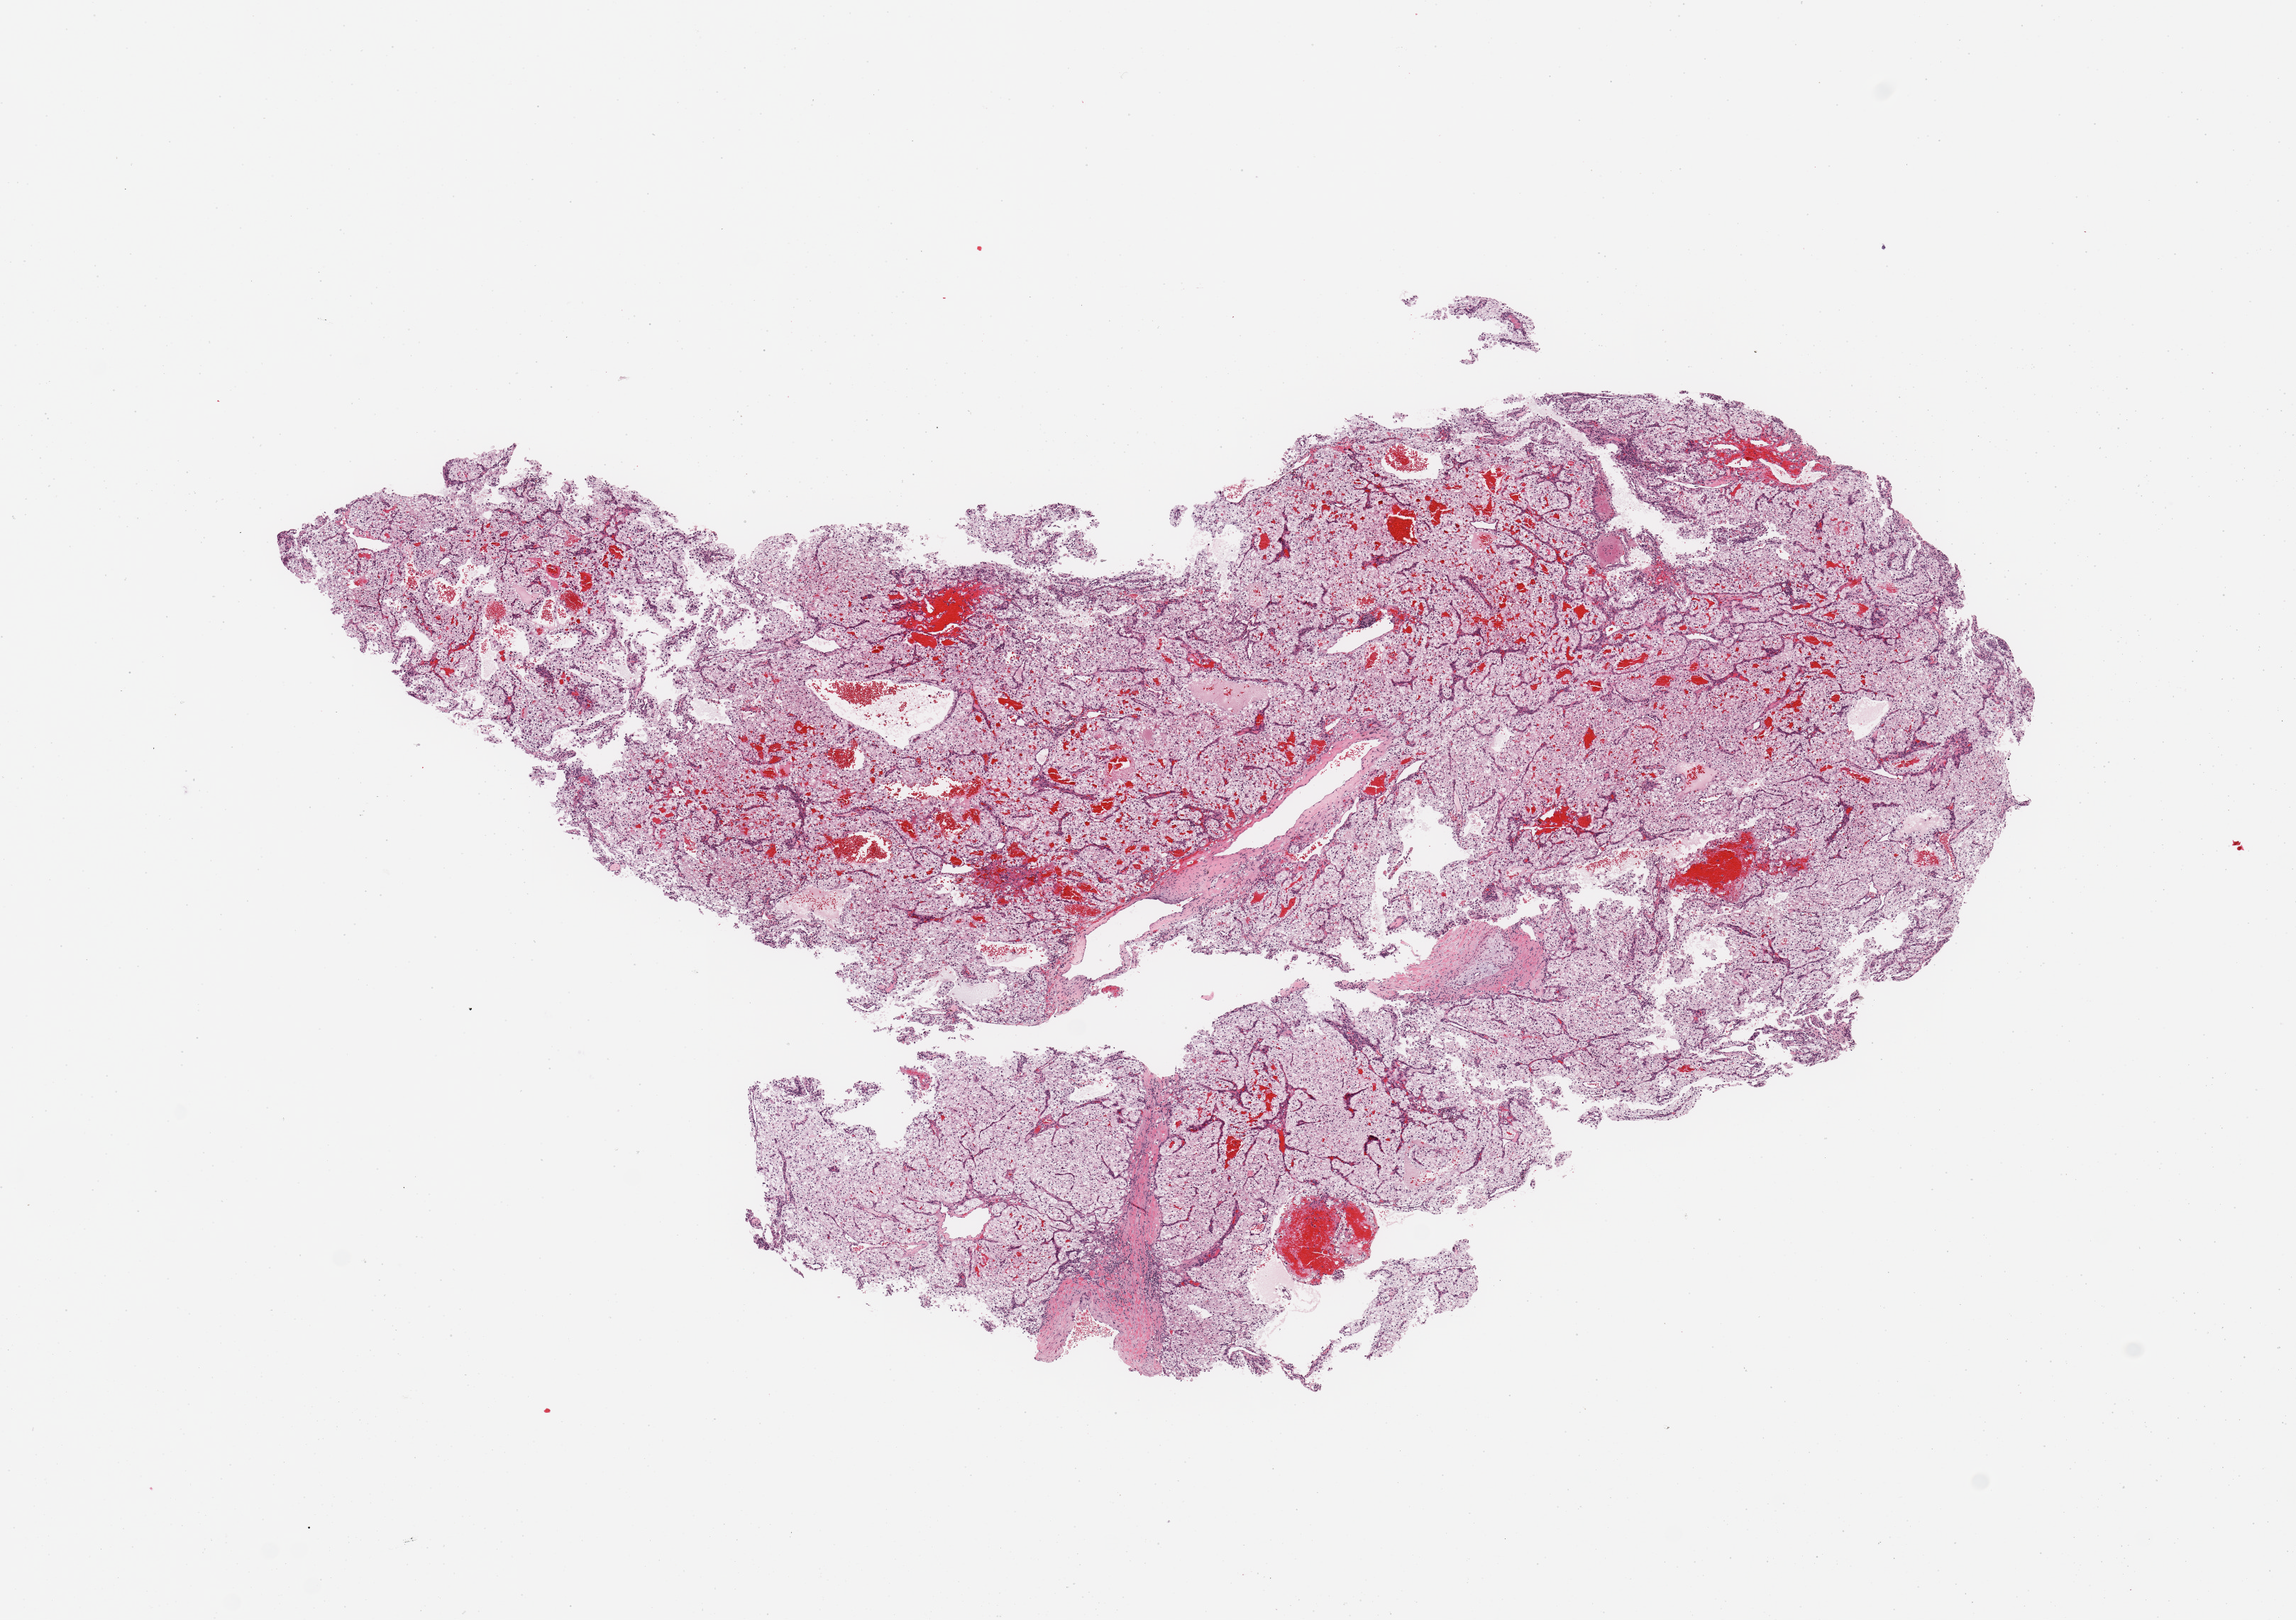
Whole-slide histology image, H&E-stained — shown as a low-resolution overview of the whole scanned area (about 12.8 x 9.0 mm, acquisition: 20x scan); kidney, tumour tissue. Female, 57 y/o. Histologic grade: G3 (poorly differentiated).
Diagnosis: Renal cell carcinoma, NOS. AJCC pathologic stage: III. Primary tumour site (as recorded): middle.